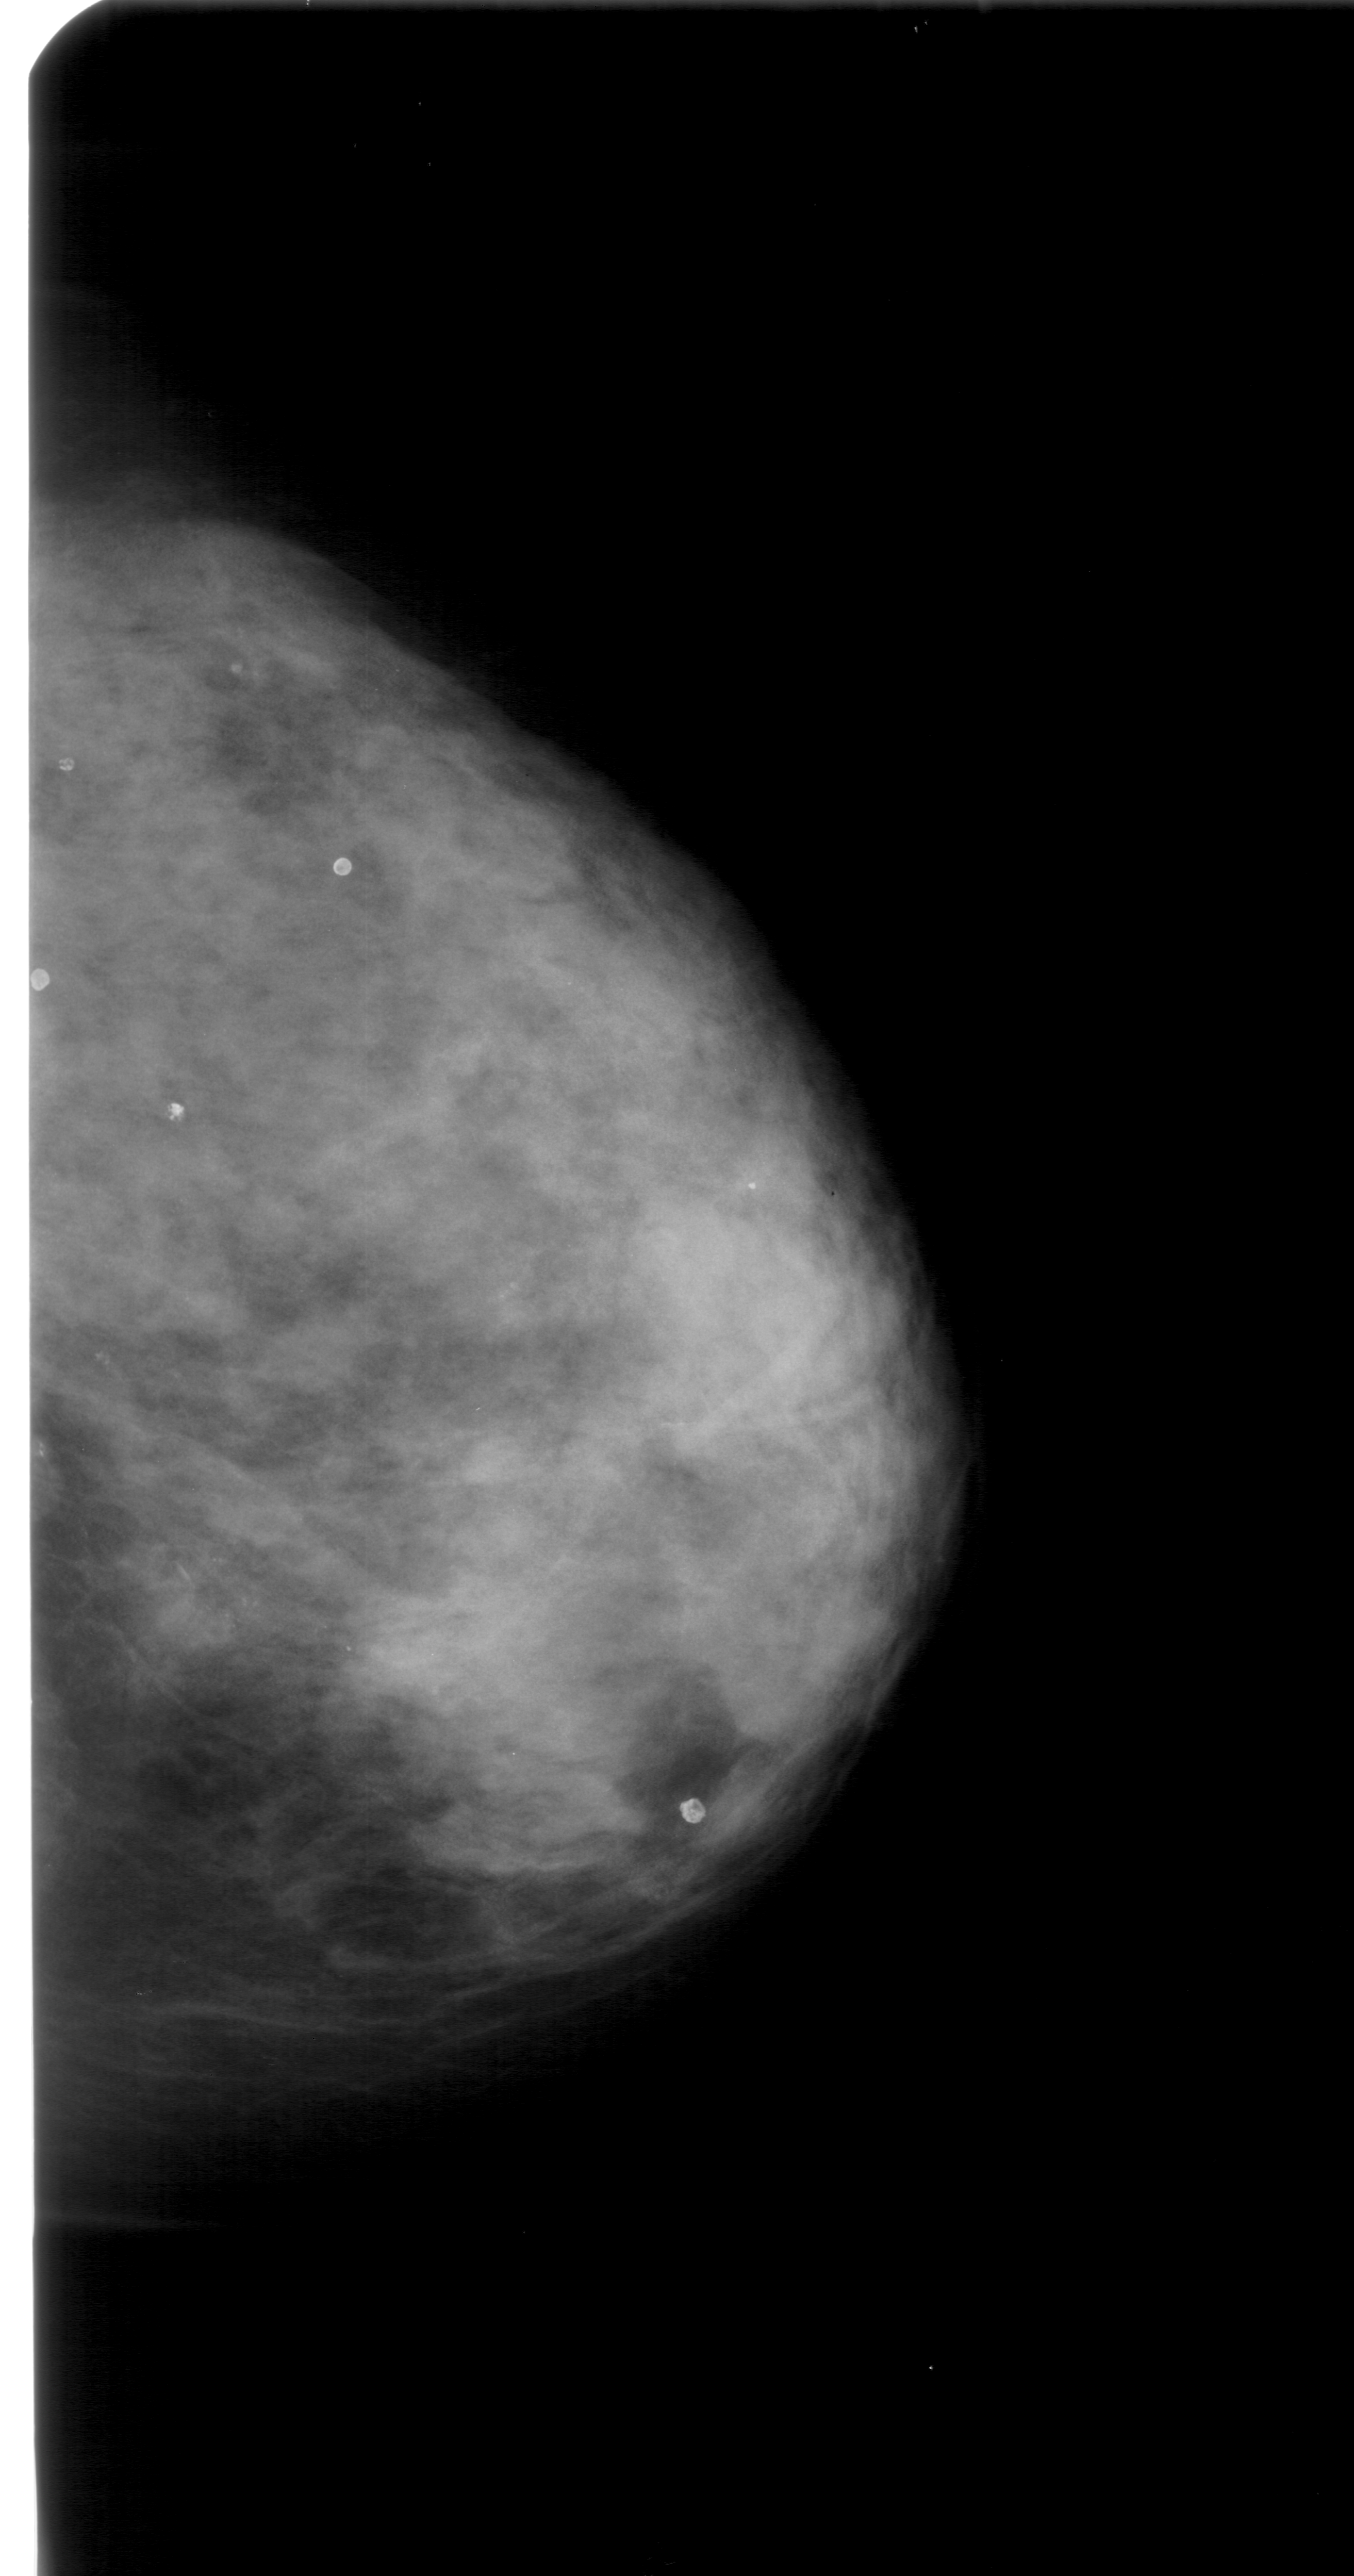
Digitized screen-film mammogram; right breast; craniocaudal (CC) view; BI-RADS breast density category 4 (scale 1–4).
Calcifications, morphology pleomorphic, distribution clustered; BI-RADS assessment category 4; subtlety rating 2 on a 1 (subtle) to 5 (obvious) scale; pathology result (as recorded, not read from the image): benign.